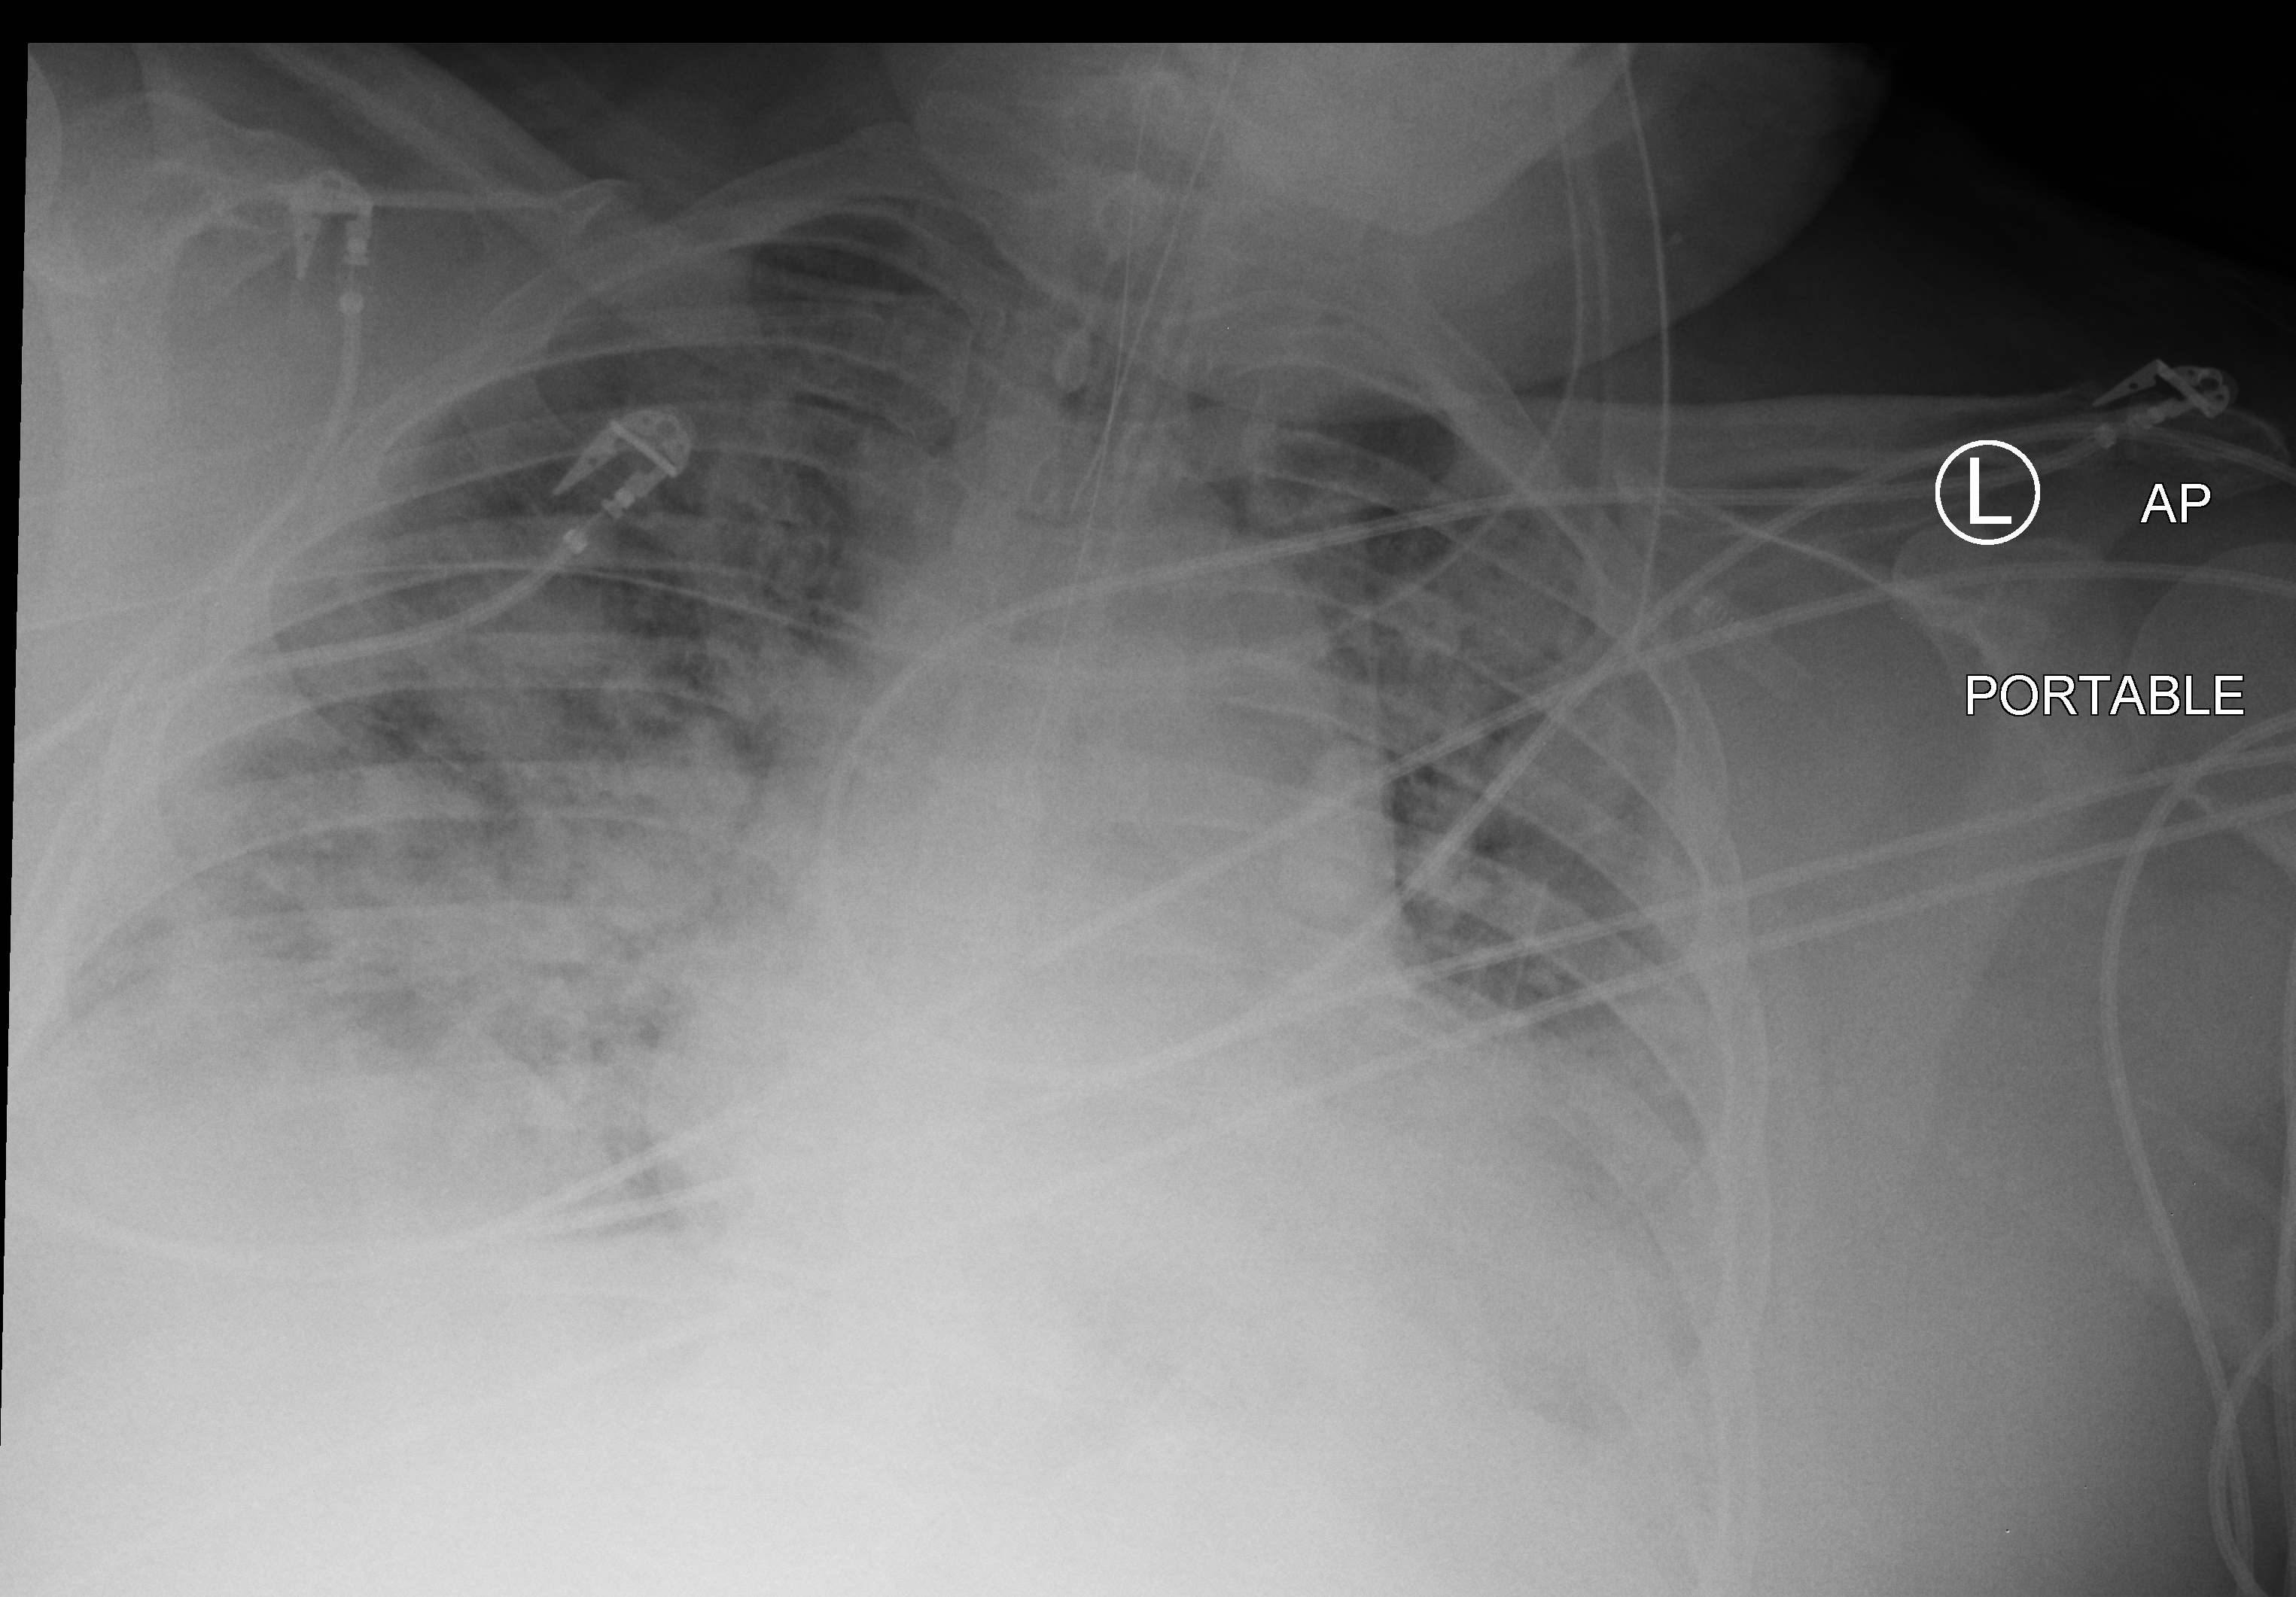
Bedside chest radiograph (computed radiography); anteroposterior (AP) projection. Patient hospitalised with COVID-19; male, aged 18–59 years.
Admission-level facts for this patient (not findings on this image; timing relative to this image not recorded): admitted to intensive care during this hospital stay: yes.